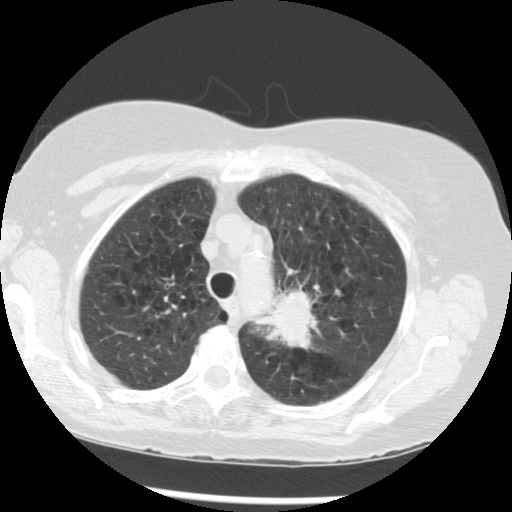
Low-dose screening chest CT, one axial slice; slice 221 of 283 in the series (ordered by position); reconstruction kernel STANDARD; lung window (W 1500 / L -600 HU); 2.5 mm slice thickness; 512 × 512 image matrix.
Annotated regions visible in this slice (manually delineated by an expert):
- lesion 1 (tumor, upper lobe of left lung): box from (x=258, y=290) to (x=317, y=348) px